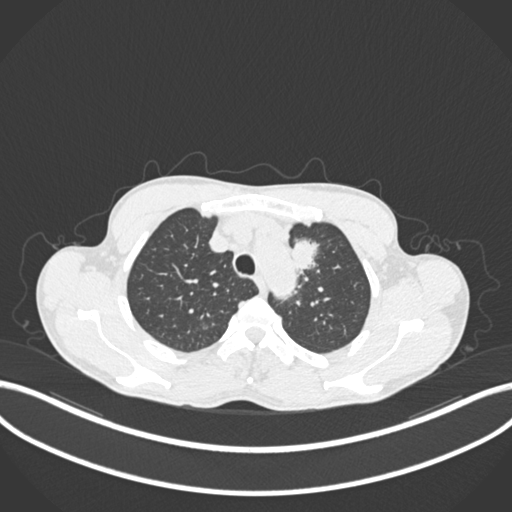
Chest CT, one axial slice; position 163 of 211 along the scan axis; reconstruction kernel B30f; 120 kVp; lung window (W 1500 / L -600 HU); 1 mm slice thickness; 512 × 512 image matrix, field of view 400 × 400 mm. Male patient, age 58 years. Case-level facts recorded for this patient, not image findings: clinical TNM (as recorded): T1c N1 M0.
Outlined on this slice (rectangle marked by the reading radiologist):
- lung tumour (recorded histology: adenocarcinoma): bounding box <286,238,328,283> (left, top, right, bottom; pixels)